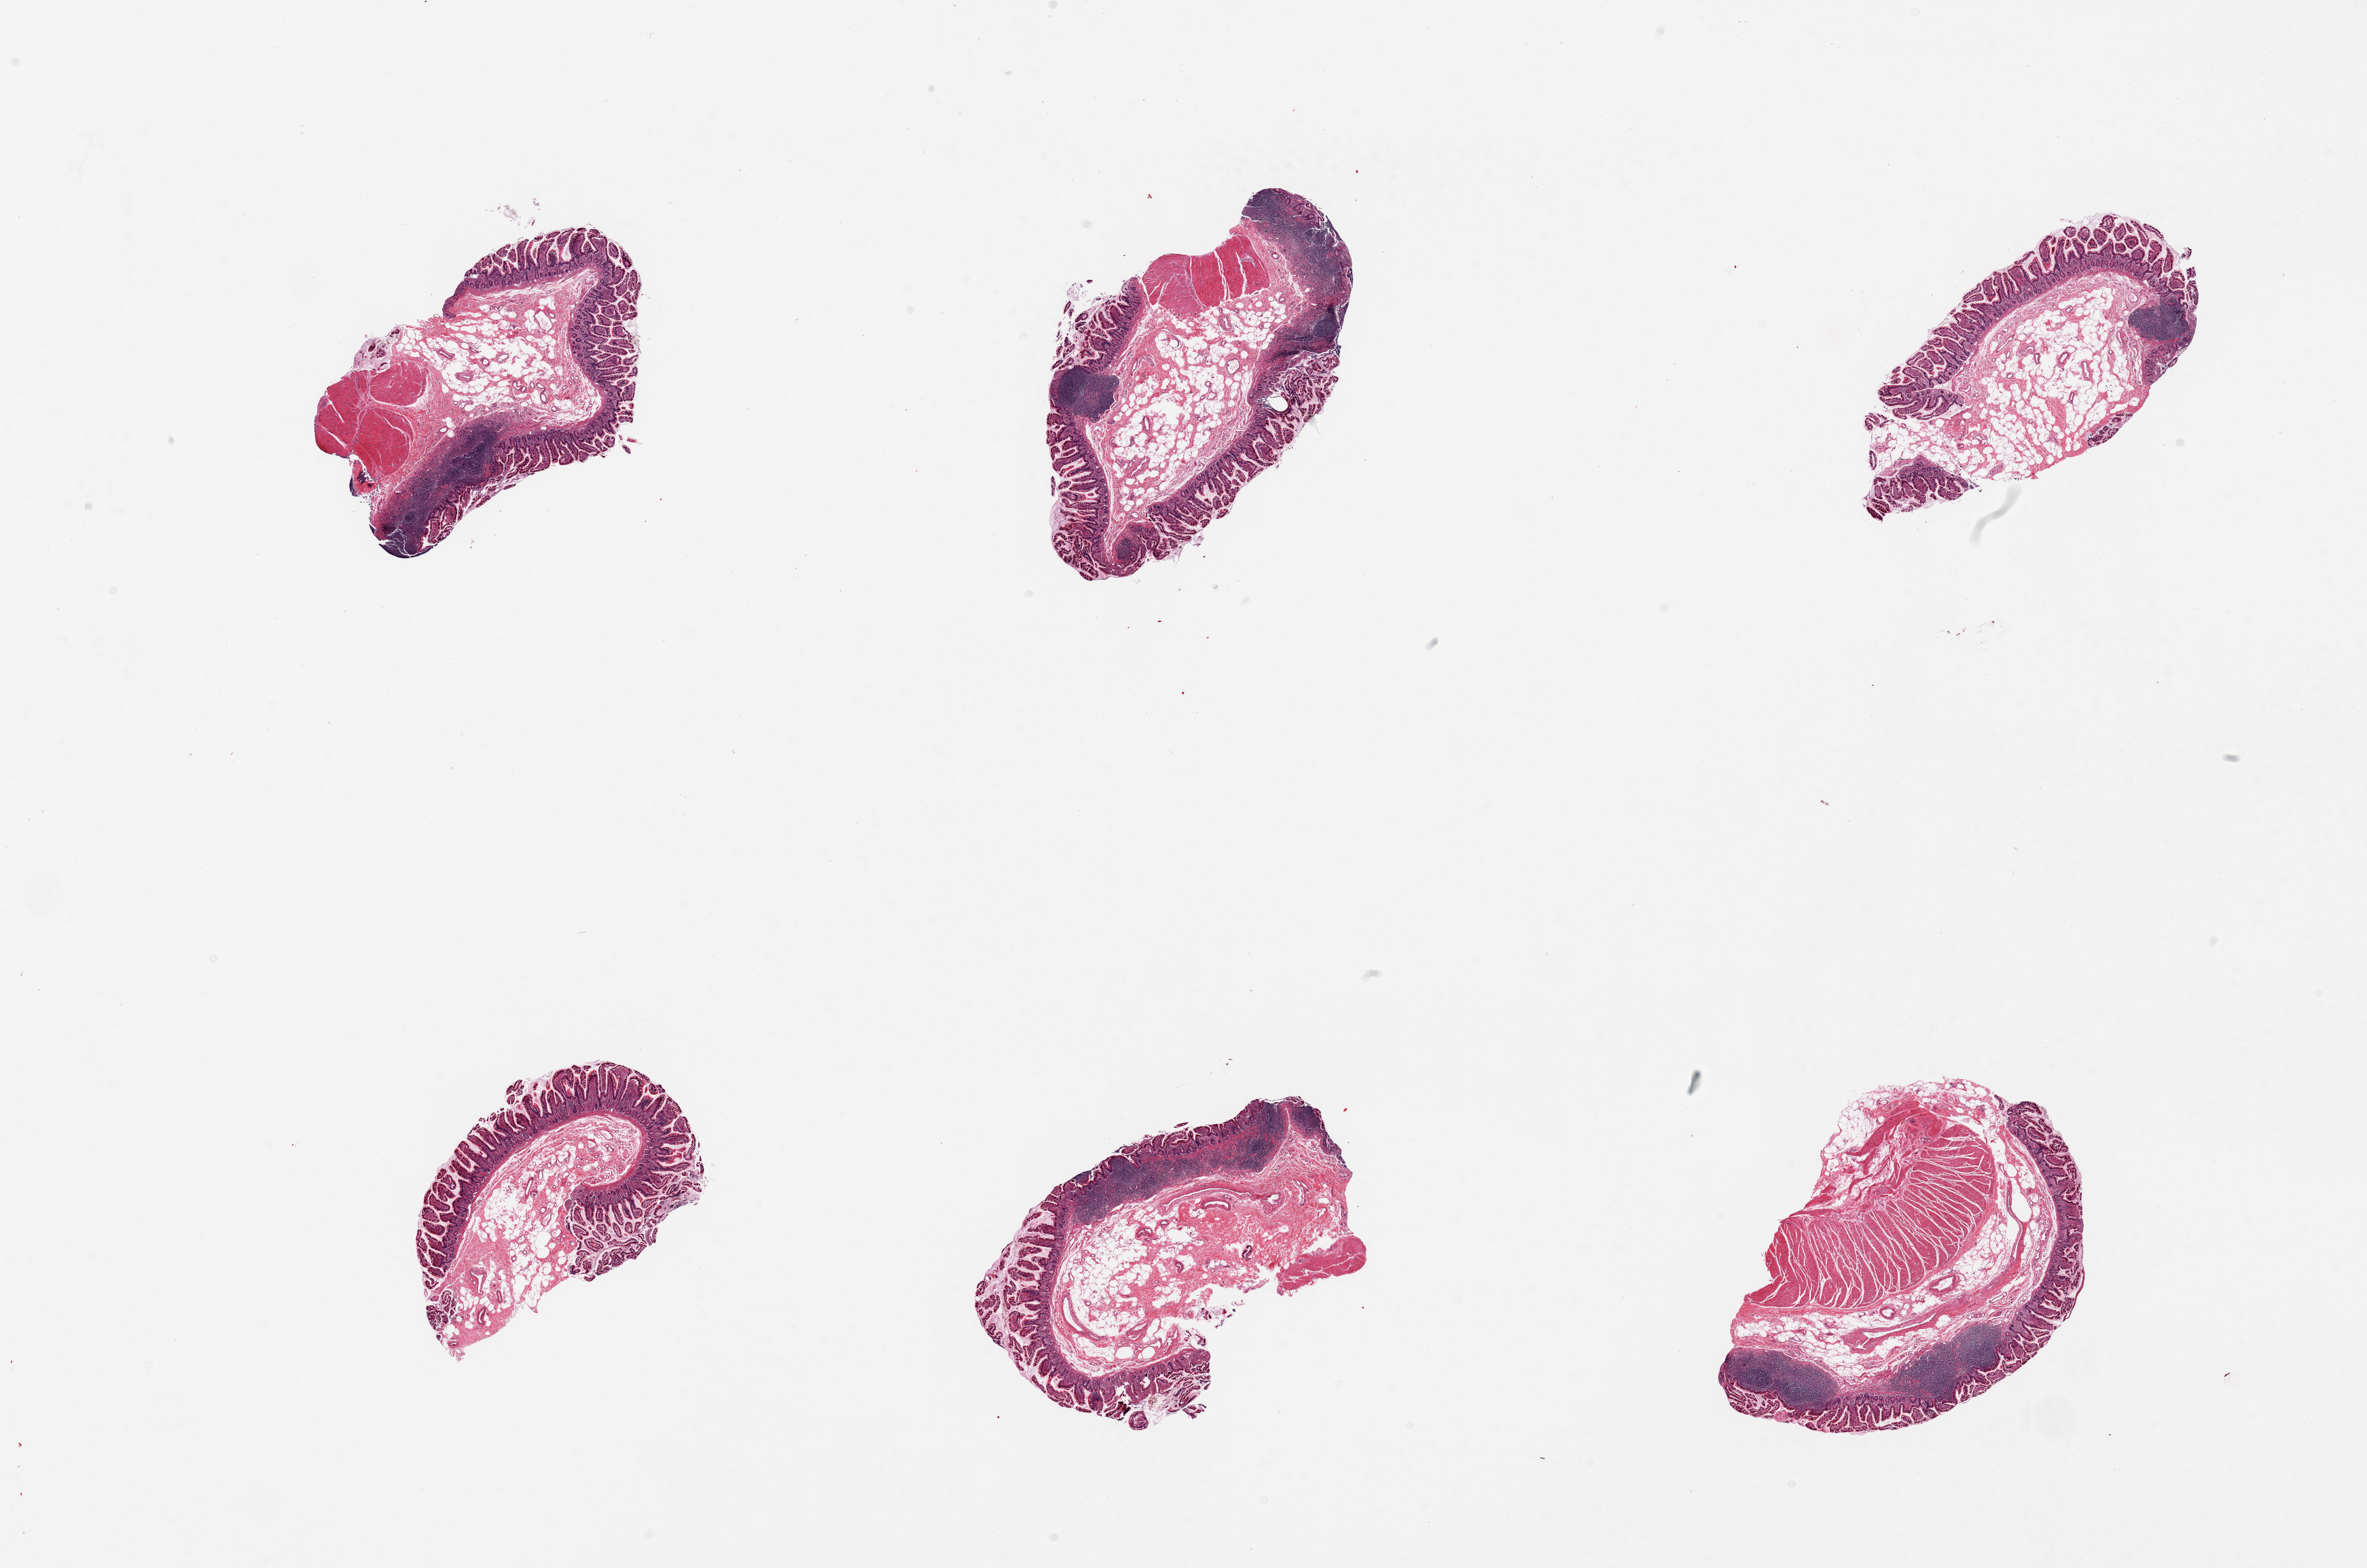
Digitized H&E-stained section, low-resolution overview of the scanned area, about 27.6 x 18.3 mm (acquisition: 20x scan), PAXgene-fixed, paraffin-embedded tissue, sampled site (target tissue): ileum, donor tissue sample.
• review note (as recorded): 6 pieces: 5 with abundant lymphoid tissues; well dissected mucosa and submucosa